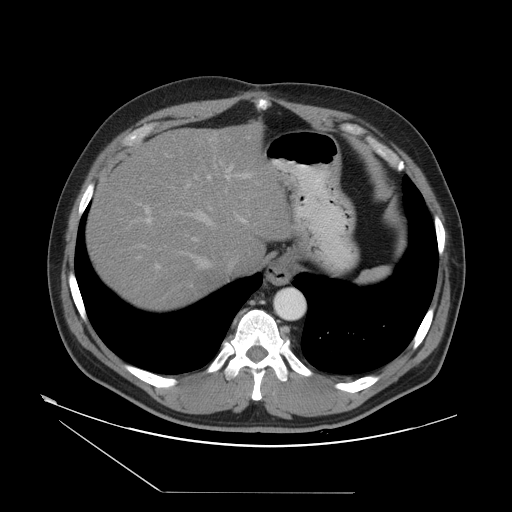
Contrast-enhanced abdominal CT, one axial slice; position 41 of 55 along the scan axis; 120 kVp; intravenous contrast given; soft-tissue window (W 400 / L 40 HU); 5 mm slice thickness; 512 × 512 image matrix, field of view 454 × 454 mm. Male patient, age 59 years. From the clinical record (not read from this slice): diagnosis: colorectal cancer liver metastases, imaged before liver resection; multiple liver metastases: yes; largest metastasis: 0.3 cm; chemotherapy before resection: yes.
Annotated regions visible in this slice (outlined manually by an expert reader):
- hepatic veins: bounding box (x1, y1, x2, y2) in pixels: (129, 190, 247, 269)
- liver: (91, 128, 289, 308)
- planned liver remnant (the part of the liver to remain after resection): (91, 153, 263, 308)
- portal vein (with intrahepatic branches): (137, 155, 252, 269)